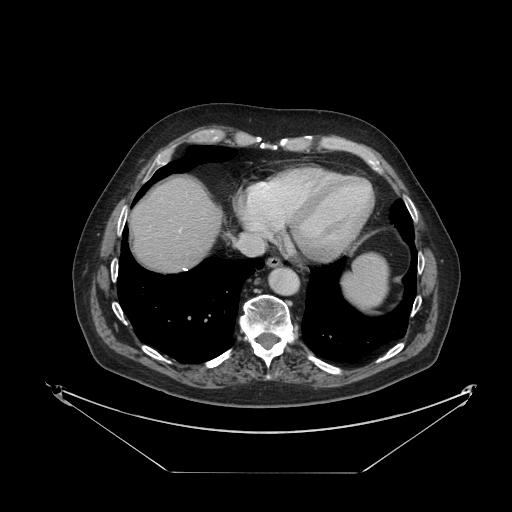
Contrast-enhanced abdominal CT, one axial slice; slice 111 of 121 in the series (ordered by position); reconstruction kernel STANDARD; intravenous contrast given; soft-tissue window (W 400 / L 40 HU); 2.5 mm slice thickness; 512 × 512 image matrix. Male patient, age 68 years. Case-level facts recorded for this patient, not image findings: diagnosis: colorectal cancer liver metastases, imaged before liver resection; multiple liver metastases: no; largest metastasis: 4 cm; disease in both lobes: no.
Annotated regions visible in this slice (manually delineated by an expert):
- liver: bounding box <132,178,220,271> (left, top, right, bottom; pixels)
- planned liver remnant (the part of the liver to remain after resection): <132,178,220,271>